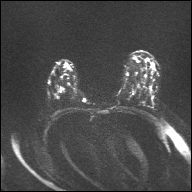
Breast MRI, one axial slice. Diffusion-weighted series; image 2 of 4 stored at this slice position (different b-values; order by instance number). 1.5 T. 4 mm slice thickness. 192 × 192 image matrix. Female patient.
Outlined on this slice (outlined manually by an expert reader):
- tumour on diffusion-weighted imaging: bounding box [x1, y1, x2, y2] px = [60, 88, 62, 91]